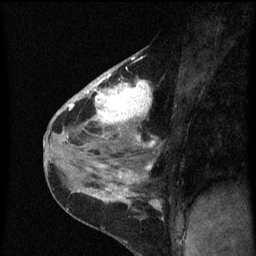
Breast MRI (dynamic contrast-enhanced), one sagittal slice; position 36 of 60 along the scan axis; dynamic contrast-enhanced series, image 2 of 3 at this slice position (ordered by acquisition); 1.5 T; TE 4.2 ms, TR 8 ms; 256 × 256 image matrix. Female patient, age 38 years.
Annotated regions visible in this slice (semi-automatic segmentation, software-assisted and operator-edited):
- analysis volume of interest (the breast-tissue region the enhancement analysis was run in; not a lesion): bounding box <80,52,159,151> (left, top, right, bottom; pixels)
- tumour enhancement mask (voxels above the 70 % enhancement threshold inside the analysis volume of interest): <80,58,155,147>